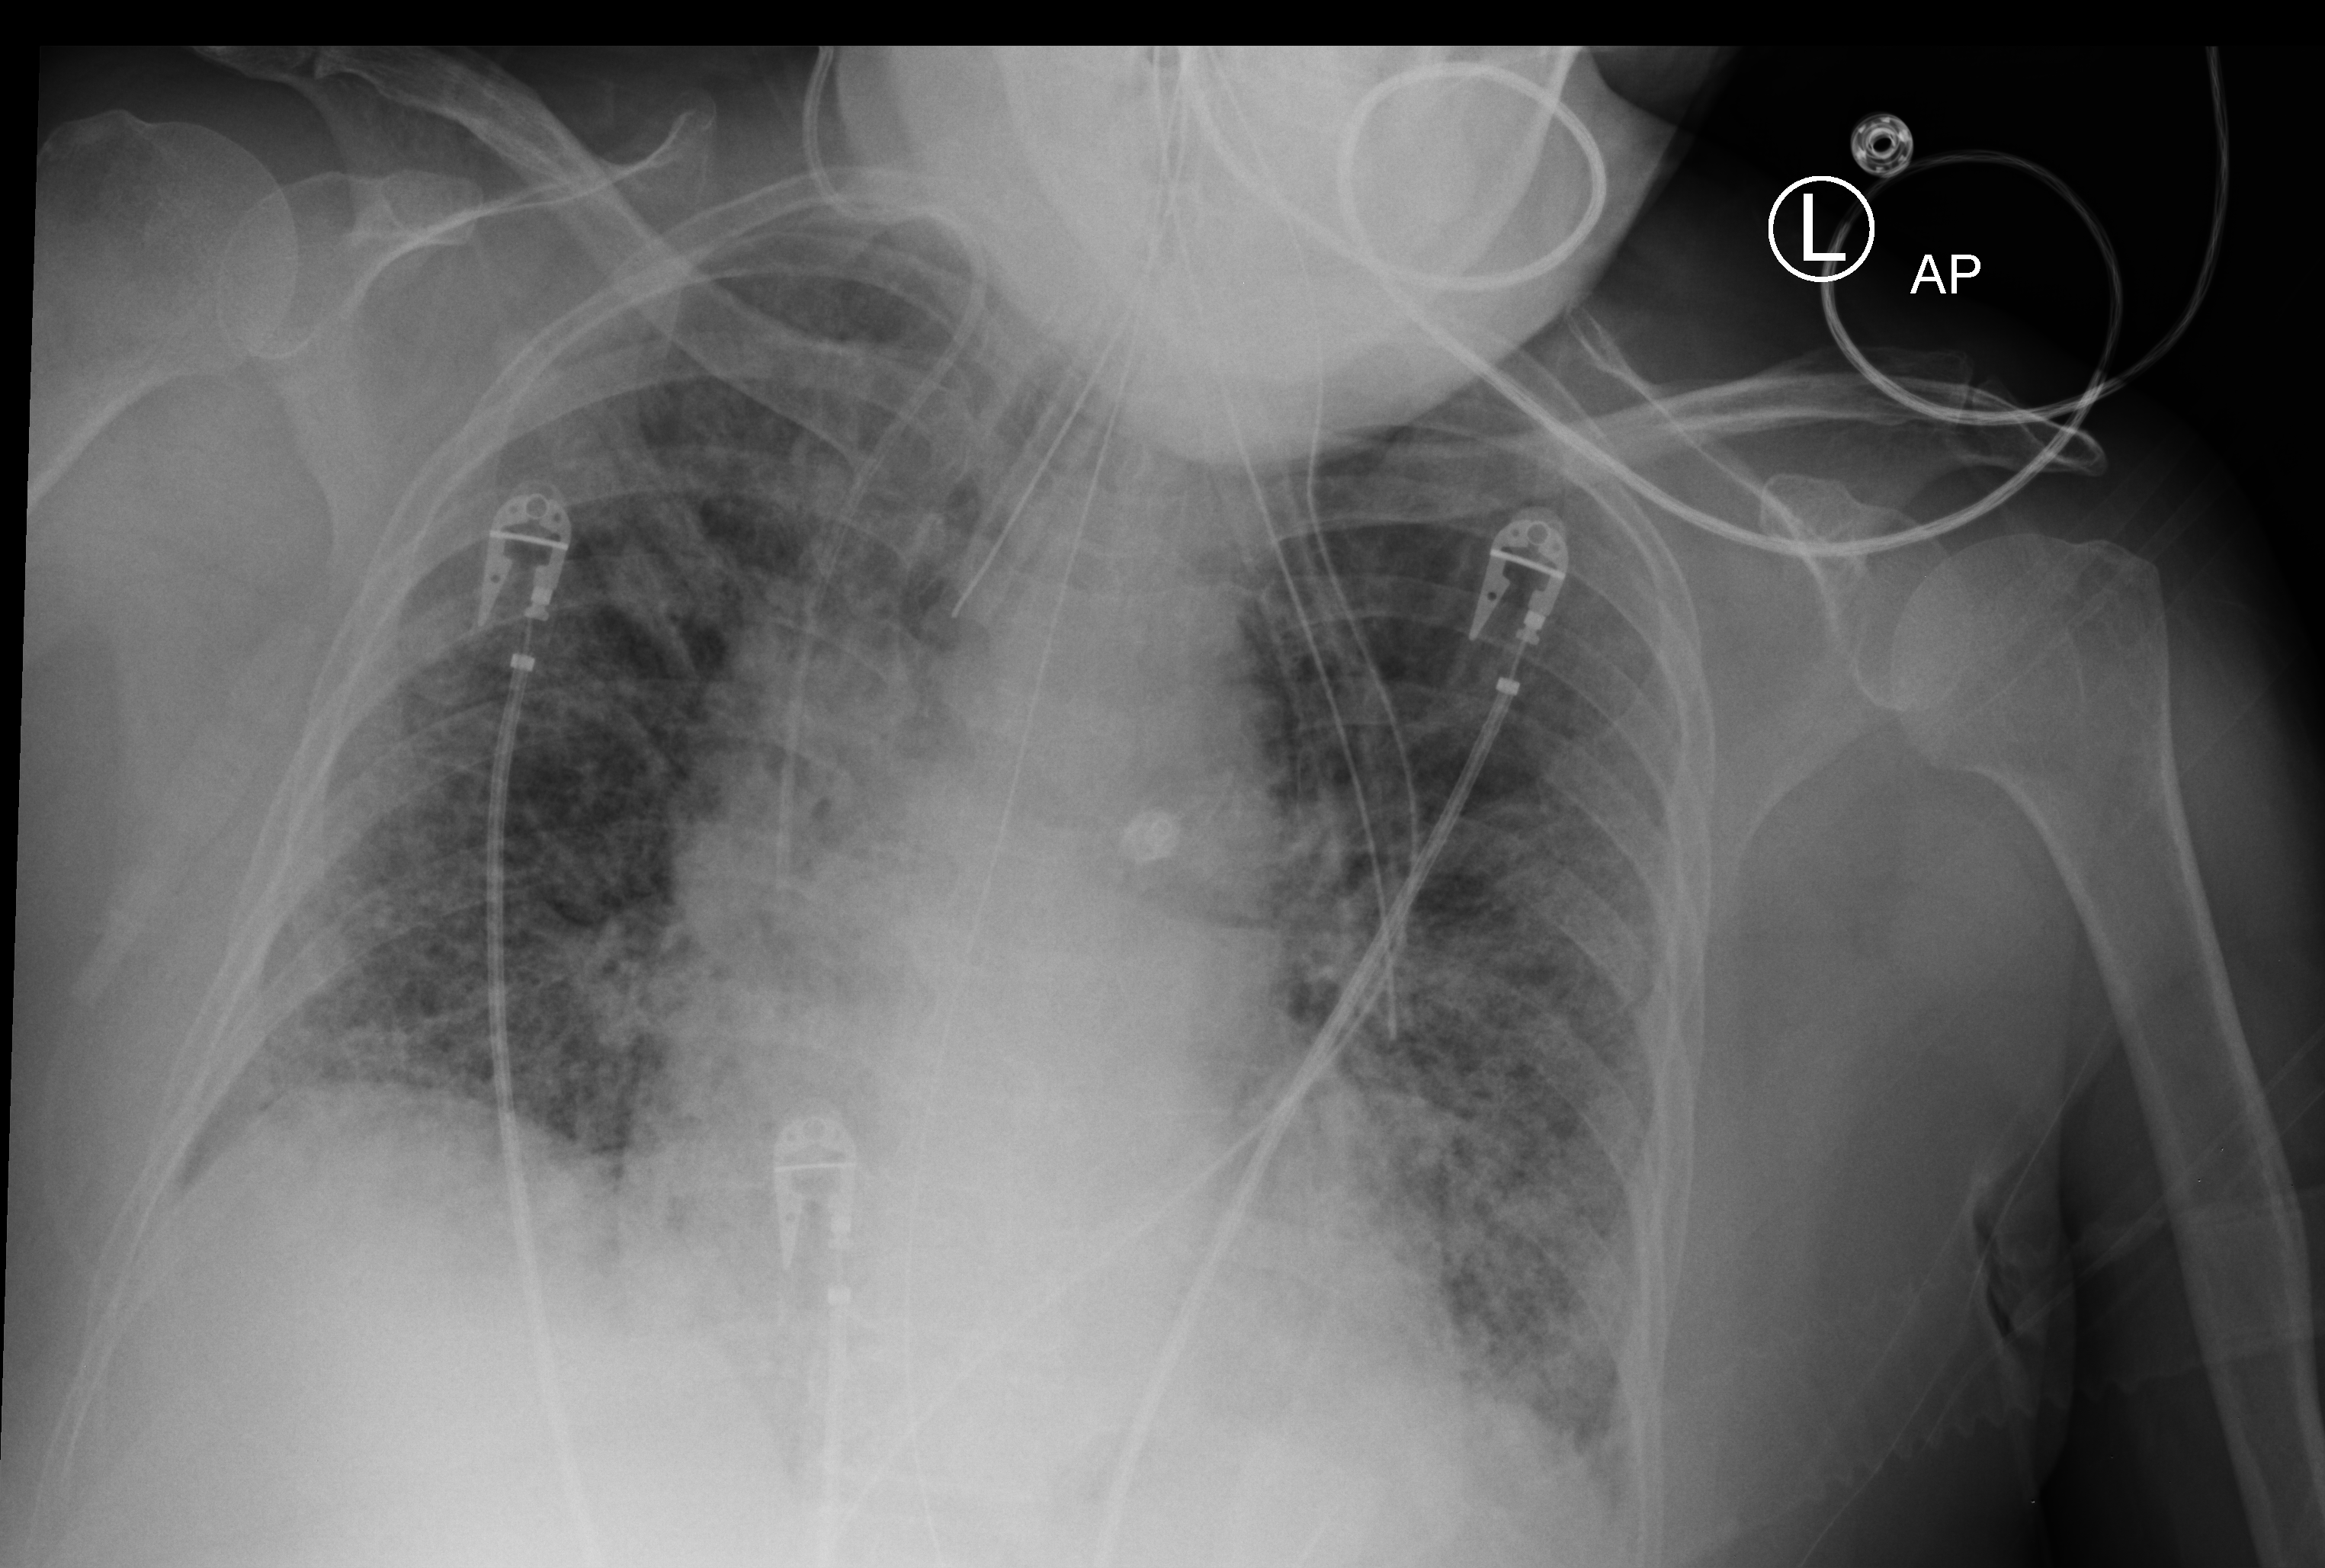
Portable chest radiograph. Female patient hospitalised with COVID-19, age 60–74 years.
Hospital-stay facts (about this admission, not read from this image; timing relative to this image not recorded): admitted to intensive care during this hospital stay: yes; mechanically ventilated during this hospital stay: yes.